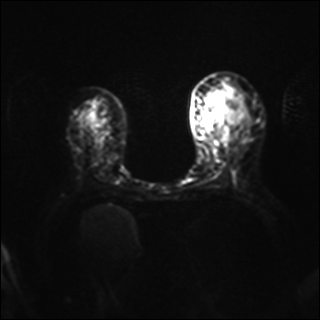
Breast MRI, one axial slice. Position 22 of 40 along the scan axis. Diffusion-weighted series; image 2 of 4 stored at this slice position (different b-values; order by instance number). 1.5 T. 4 mm slice thickness. 320 × 320 image matrix. Female patient.
Annotated regions visible in this slice (expert manual segmentation):
- tumour on diffusion-weighted imaging: bounding box <228,102,237,110> (left, top, right, bottom; pixels)